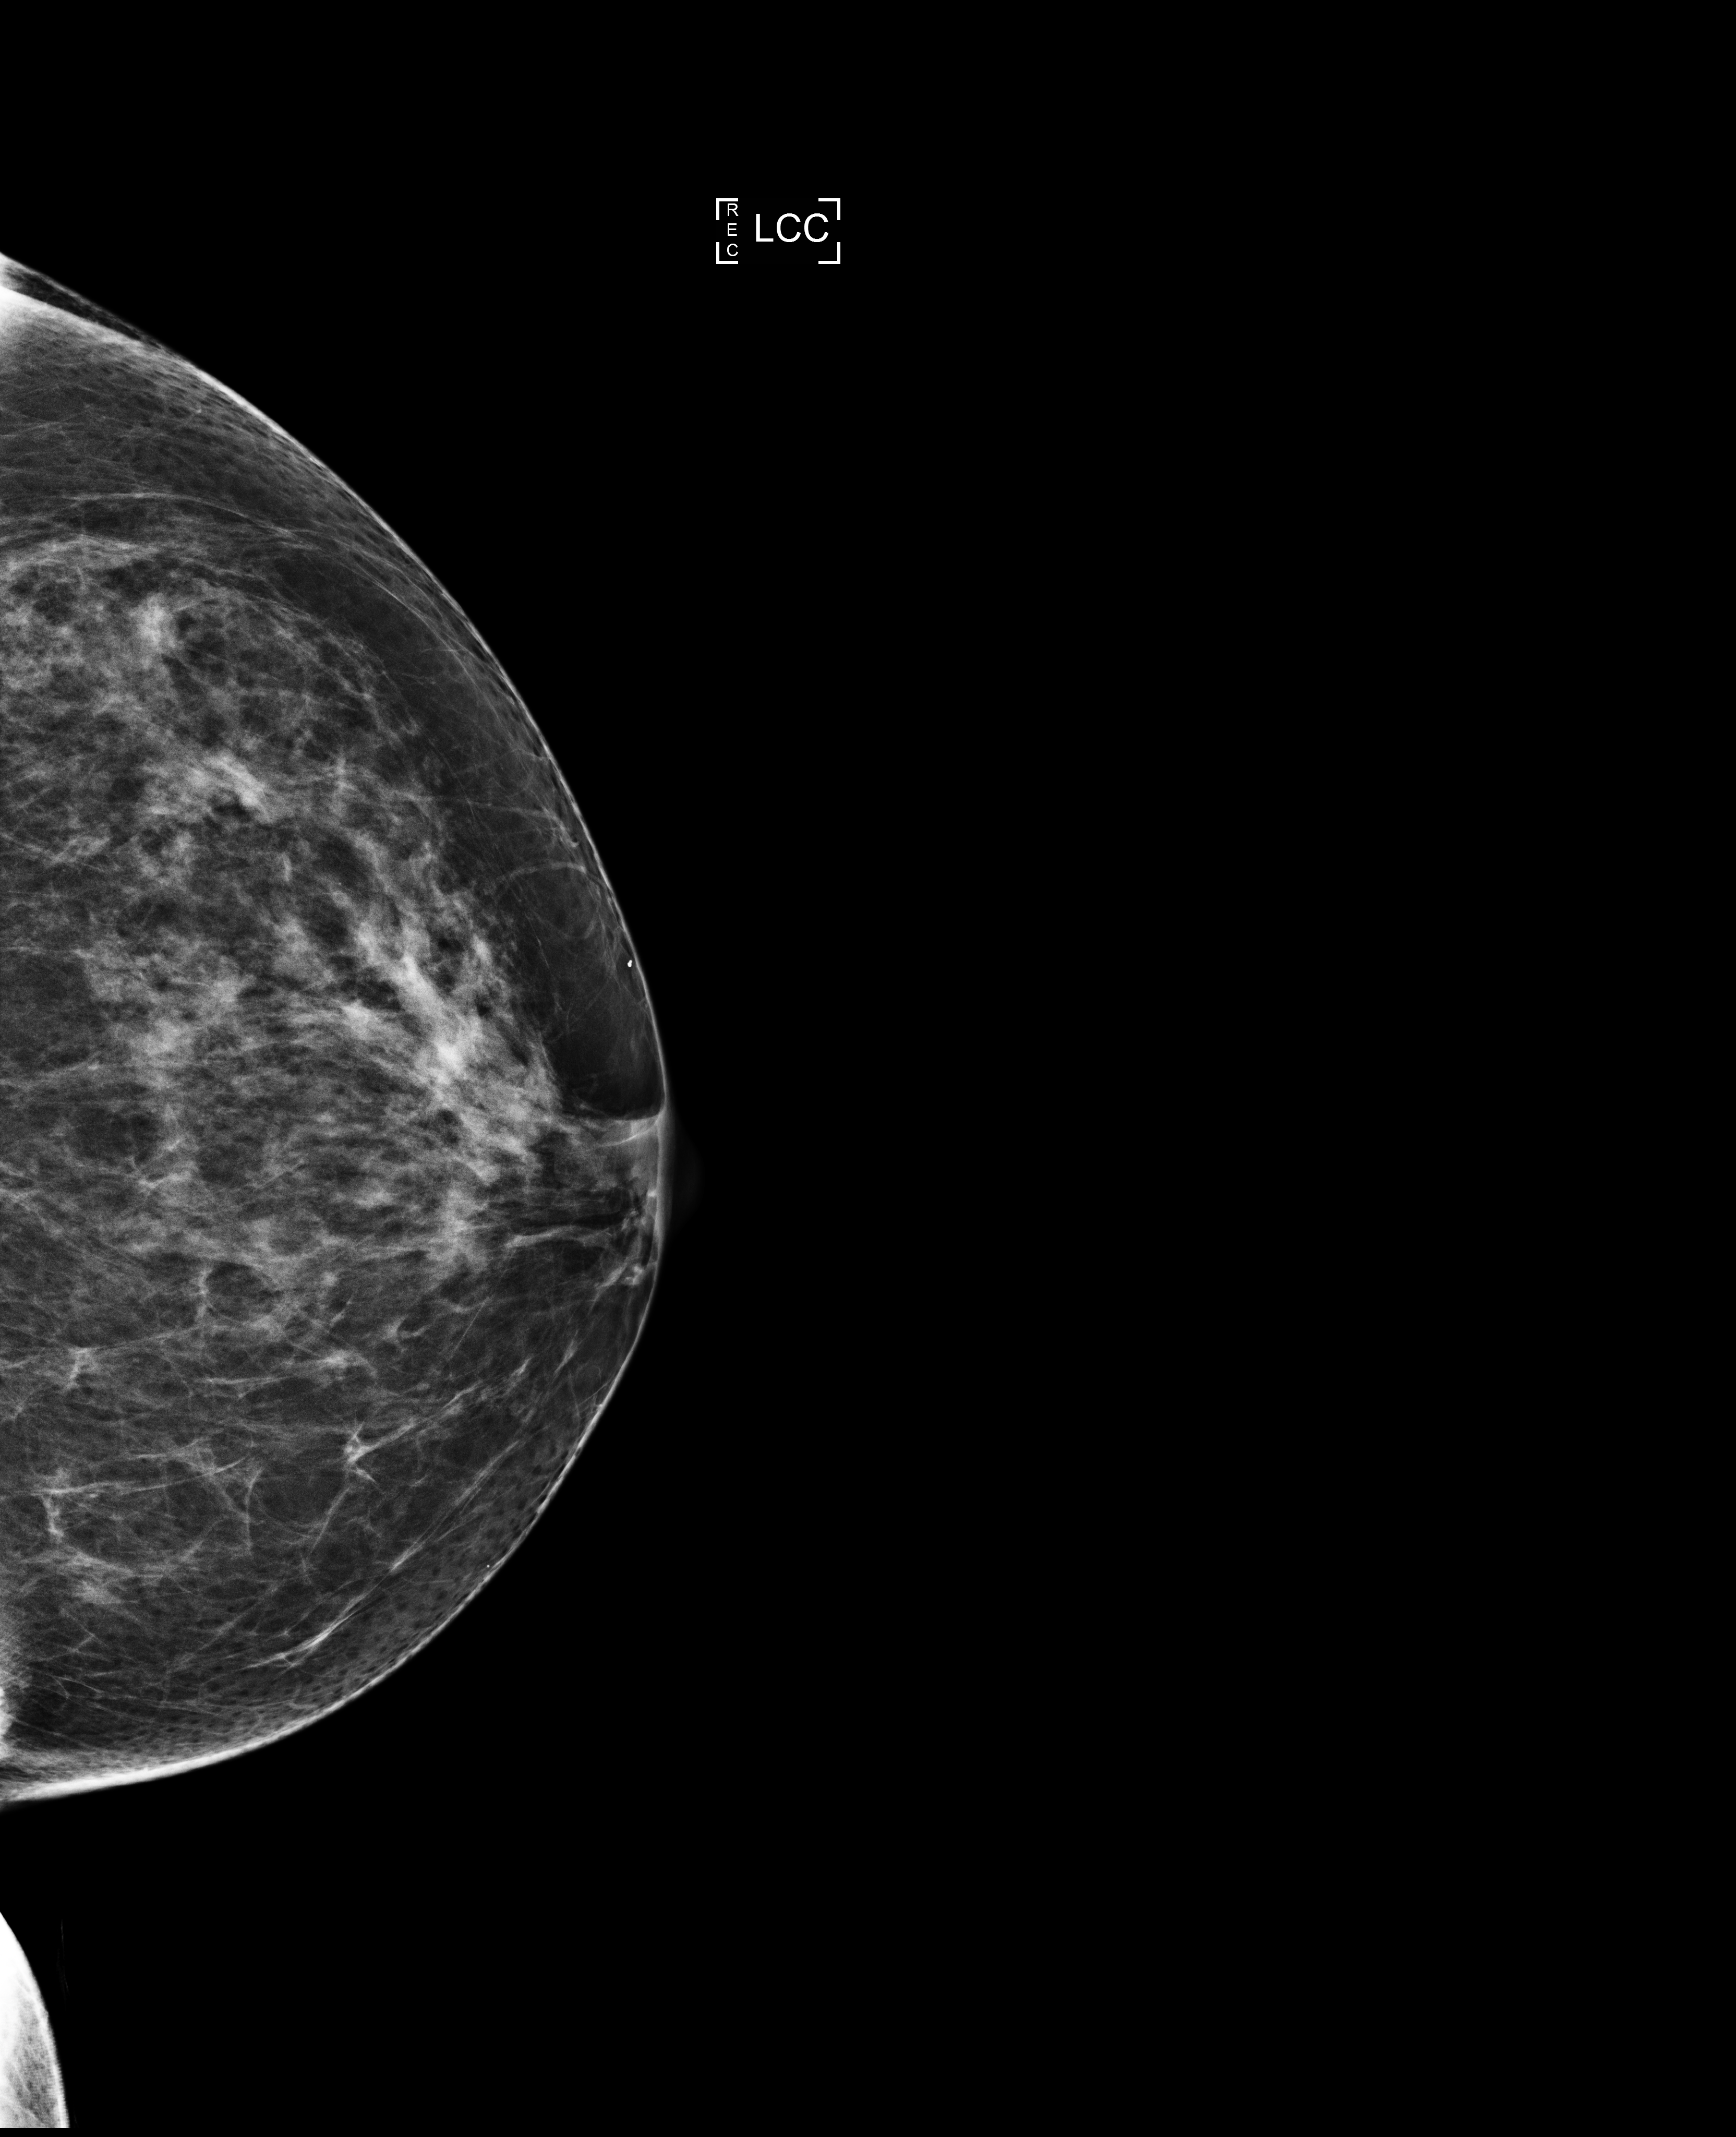
Screening examination; system: Selenia Dimensions. Patient: female, 53 years.
Image type: full-field digital mammogram. Breast: left. Projection: cranio-caudal projection.